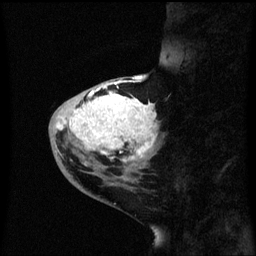
Breast MRI (dynamic contrast-enhanced), one sagittal slice. Slice 21 of 60 in the series (ordered by position). Dynamic contrast-enhanced series, image 2 of 3 at this slice position (ordered by acquisition). 1.5 T. TE 4.2 ms, TR 8.4 ms. 2.3 mm slice thickness. 256 × 256 image matrix, field of view 200 × 200 mm. Patient: female, 46 years. From the clinical record (not read from this slice): setting: breast cancer imaged before/during neoadjuvant chemotherapy; receptor status: HER2-positive.
Outlined on this slice (semi-automatic segmentation, software-assisted and operator-edited):
- analysis volume of interest (the breast-tissue region the enhancement analysis was run in; not a lesion): bounding box [x1, y1, x2, y2] px = [50, 86, 161, 171]
- tumour enhancement mask (voxels above the 70 % enhancement threshold inside the analysis volume of interest): [58, 88, 155, 163]